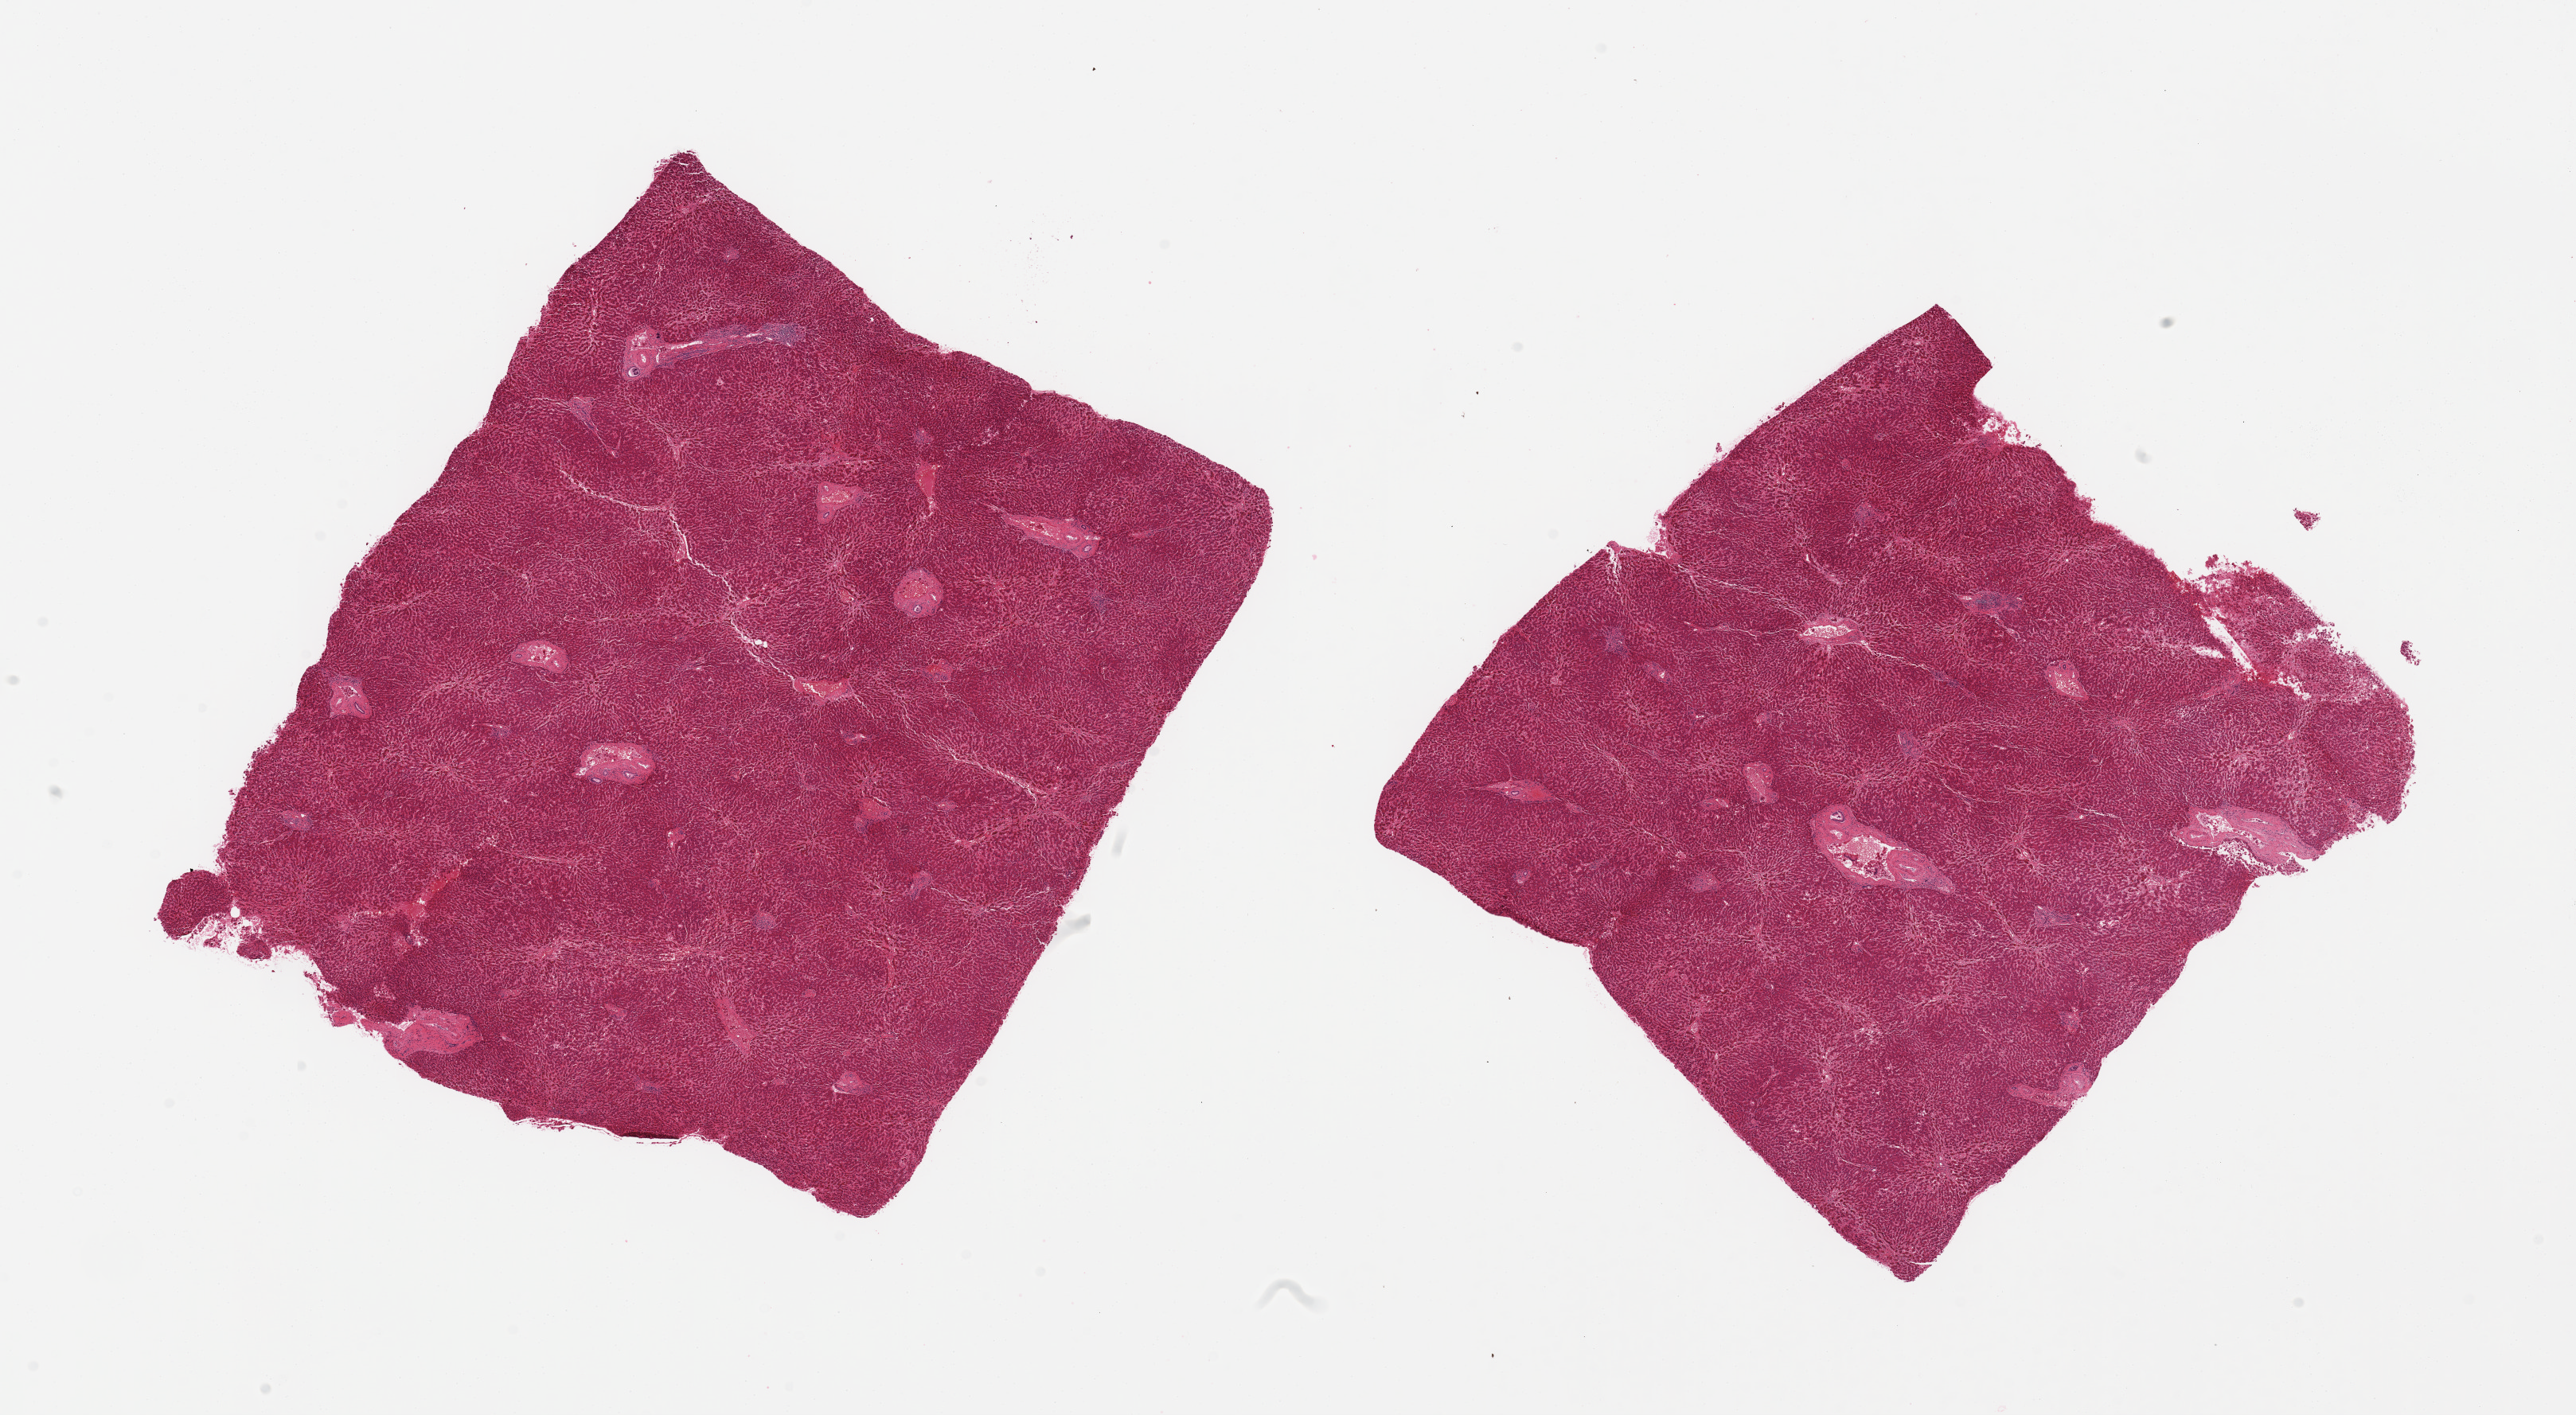
Digitized hematoxylin and eosin (H&E)-stained section, brightfield — low-resolution overview of the scanned area, about 25.6 x 14.1 mm (slide scanned at 20x); PAXgene-fixed, paraffin-embedded tissue; target tissue: liver; tissue donor sample.
Pathologist's review note for this sample: 2 pieces; central congestion.